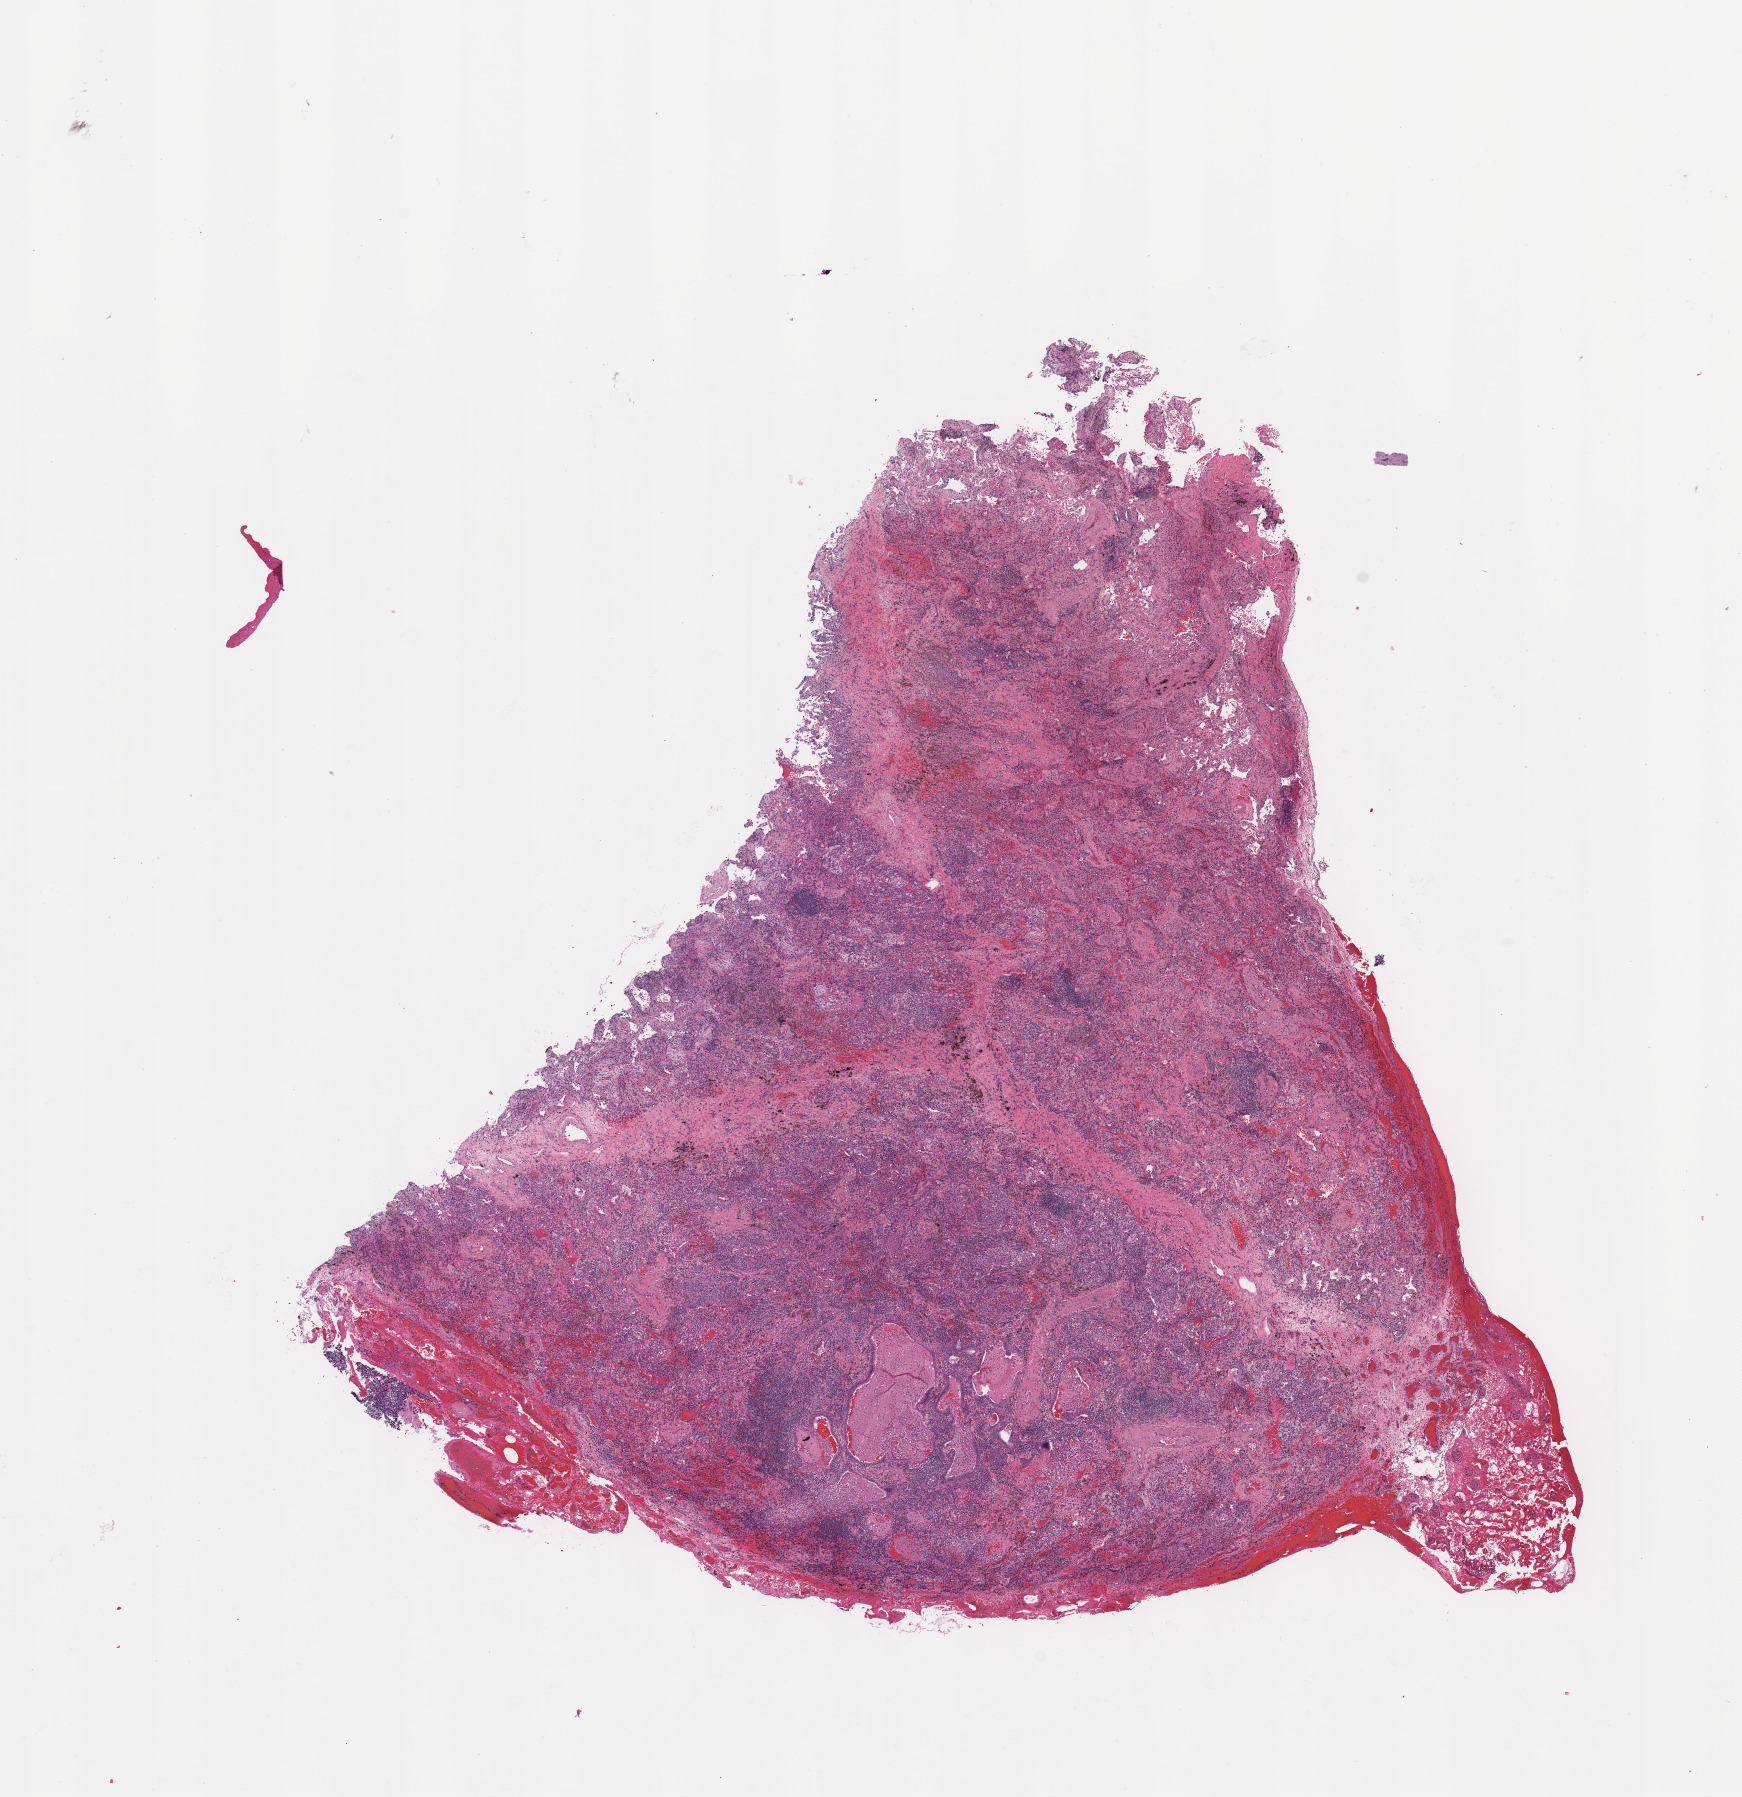
Digitized H&E tissue section (whole slide), a low-resolution overview of the entire scanned area, about 13.8 x 14.2 mm. Normal (non-tumour) tissue sample, lung. 63-year-old male patient.
- this section: normal (non-tumour) tissue from the same patient
- patient diagnosis: Squamous cell carcinoma, NOS